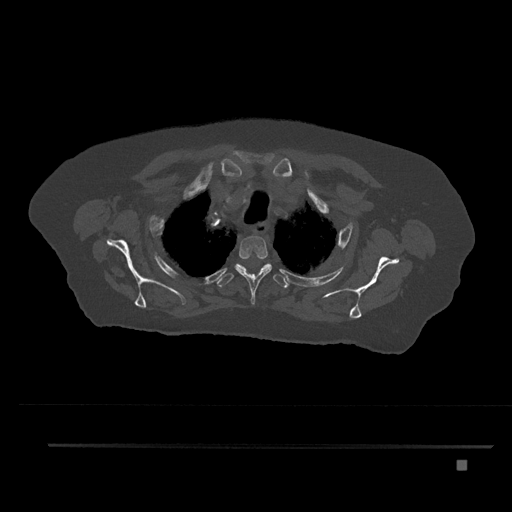
CT including the spine, one axial slice; slice 658 of 797 in the series (ordered by position); reconstruction kernel Br40s/3; bone window (W 1800 / L 400 HU); 512 × 512 image matrix, field of view 437 × 437 mm. Patient: female, 76 years. Case-level facts recorded for this patient, not image findings: primary cancer: lung.
Outlined on this slice (semi-automatic segmentation, software-assisted and operator-edited):
- T2 vertebra: box from (x=234, y=231) to (x=272, y=305) px
- T3 vertebra: (x=217, y=263)–(x=288, y=288)